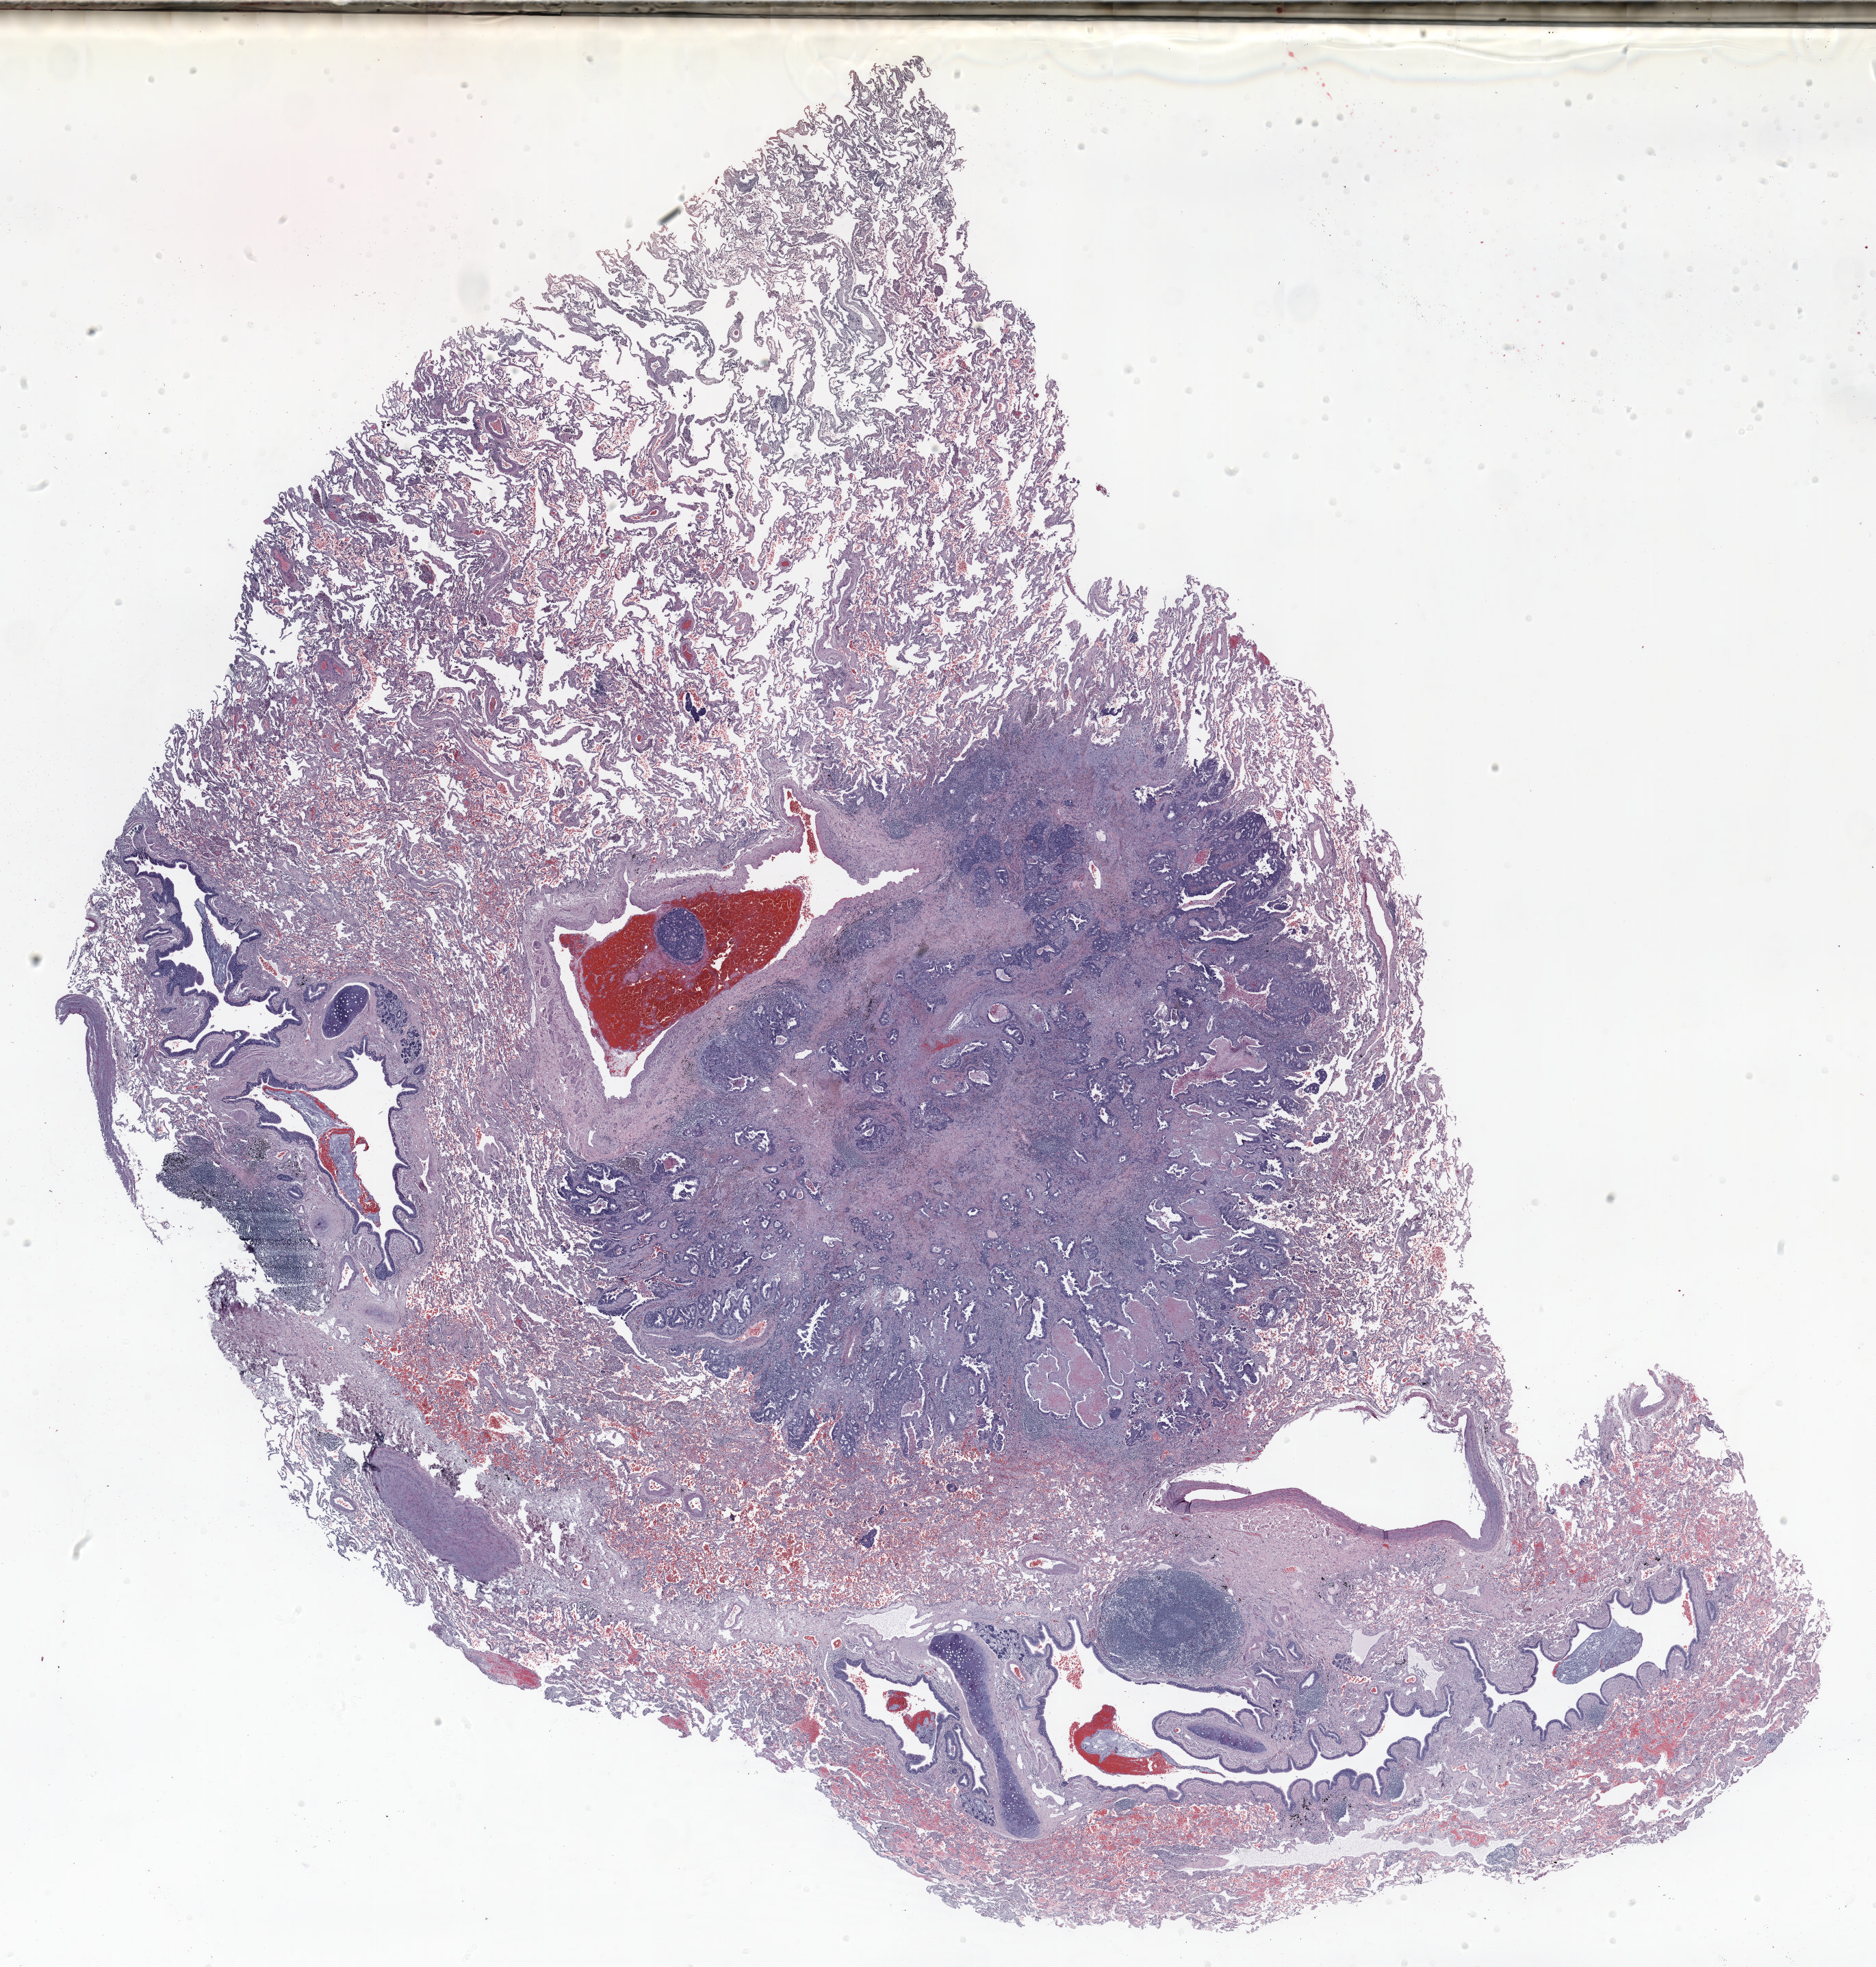
Hematoxylin and eosin (H&E) stained whole-slide image — a low-resolution overview of the entire scanned area, about 22.0 x 23.1 mm; formalin-fixed paraffin-embedded (FFPE) section; lung. Male, age 68 at enrolment. Grade: moderately differentiated (G2).
Primary tumour location (clinical record): right upper lobe. Stage (AJCC 6th edition): IA. Tumour size (pathology): 13 mm. Participant's lung-cancer diagnosis: Adenocarcinoma, NOS.